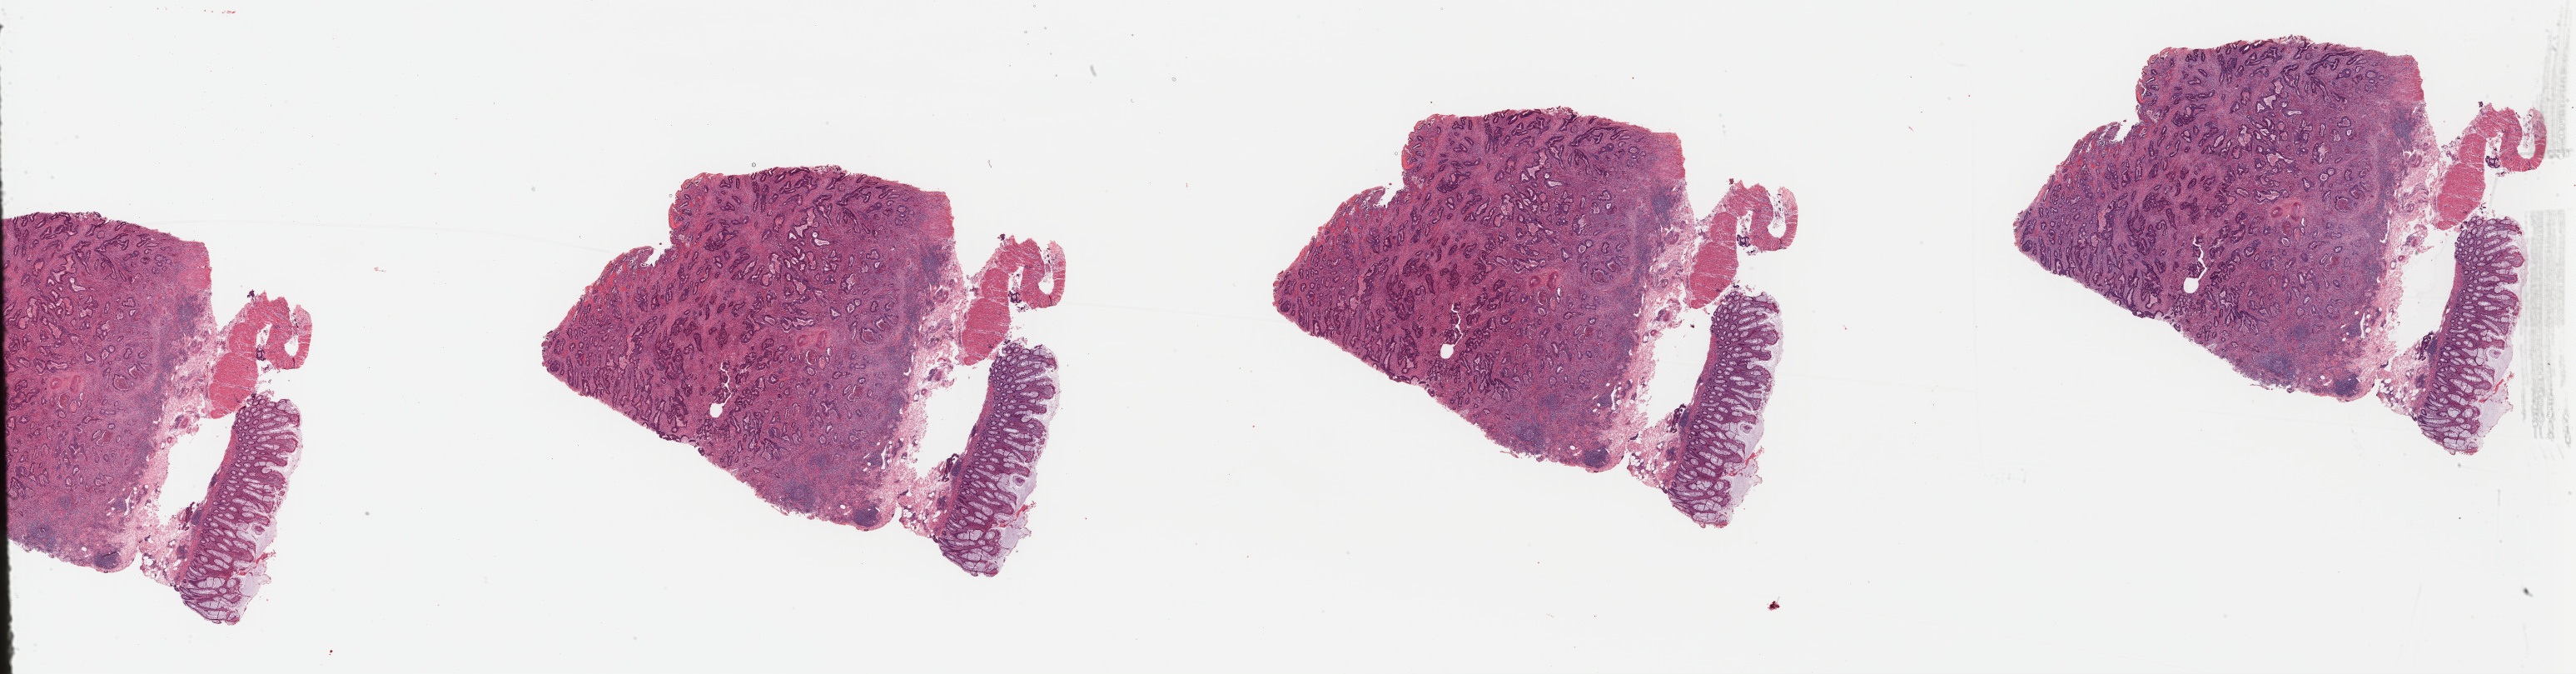
Hematoxylin and eosin (H&E) stained whole-slide image, whole scanned area (about 48.6 x 12.7 mm, from a 40x scan) shown as a low-resolution overview. Formalin-fixed paraffin-embedded (FFPE) diagnostic section. Sample: primary tumour, rectum. Patient: male, age at initial diagnosis 56 years.
Diagnosis: Adenocarcinoma, NOS (rectosigmoid junction). TNM: T3 N0 M0. Lymph nodes positive (case pathology): 0 of 44 examined. AJCC pathologic stage: IIA (6th edition).